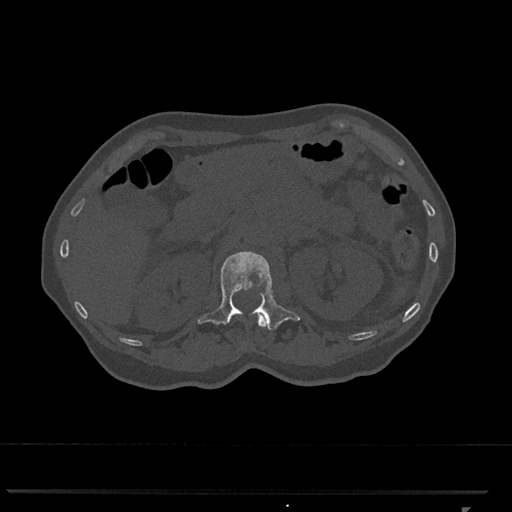
CT including the spine, one axial slice. Slice 413 of 793 in the series (ordered by position). 120 kVp. Bone window (W 1800 / L 400 HU). 512 × 512 image matrix. Female patient, age 62 years. From the clinical record (not read from this slice): primary cancer: renal.
Outlined on this slice (semi-automatic segmentation, software-assisted and operator-edited):
- L1 vertebra: box from (x=198, y=251) to (x=300, y=330) px
- T12 vertebra: (x=257, y=315)–(x=266, y=327)